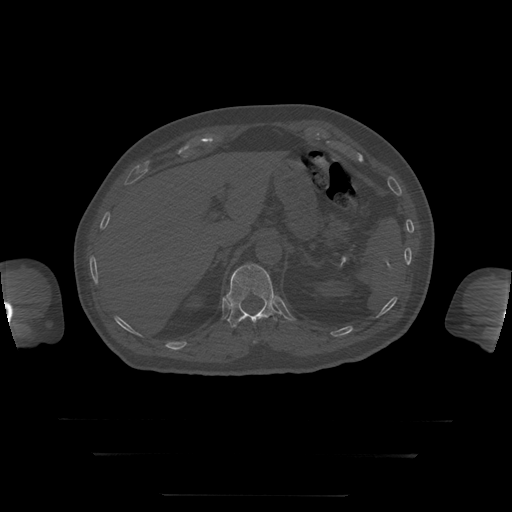
CT including the spine, one axial slice. Slice 78 of 397 in the series (ordered by position). Bone window (W 1800 / L 400 HU). 1.25 mm slice thickness. 512 × 512 image matrix, field of view 510 × 510 mm. Patient age 73 years. Case-level facts recorded for this patient, not image findings: primary cancer: prostate.
Annotated regions visible in this slice (semi-automatic segmentation, software-assisted and operator-edited):
- T11 vertebra: bounding box <254,341,257,343> (left, top, right, bottom; pixels)
- T12 vertebra: <227,264,282,328>